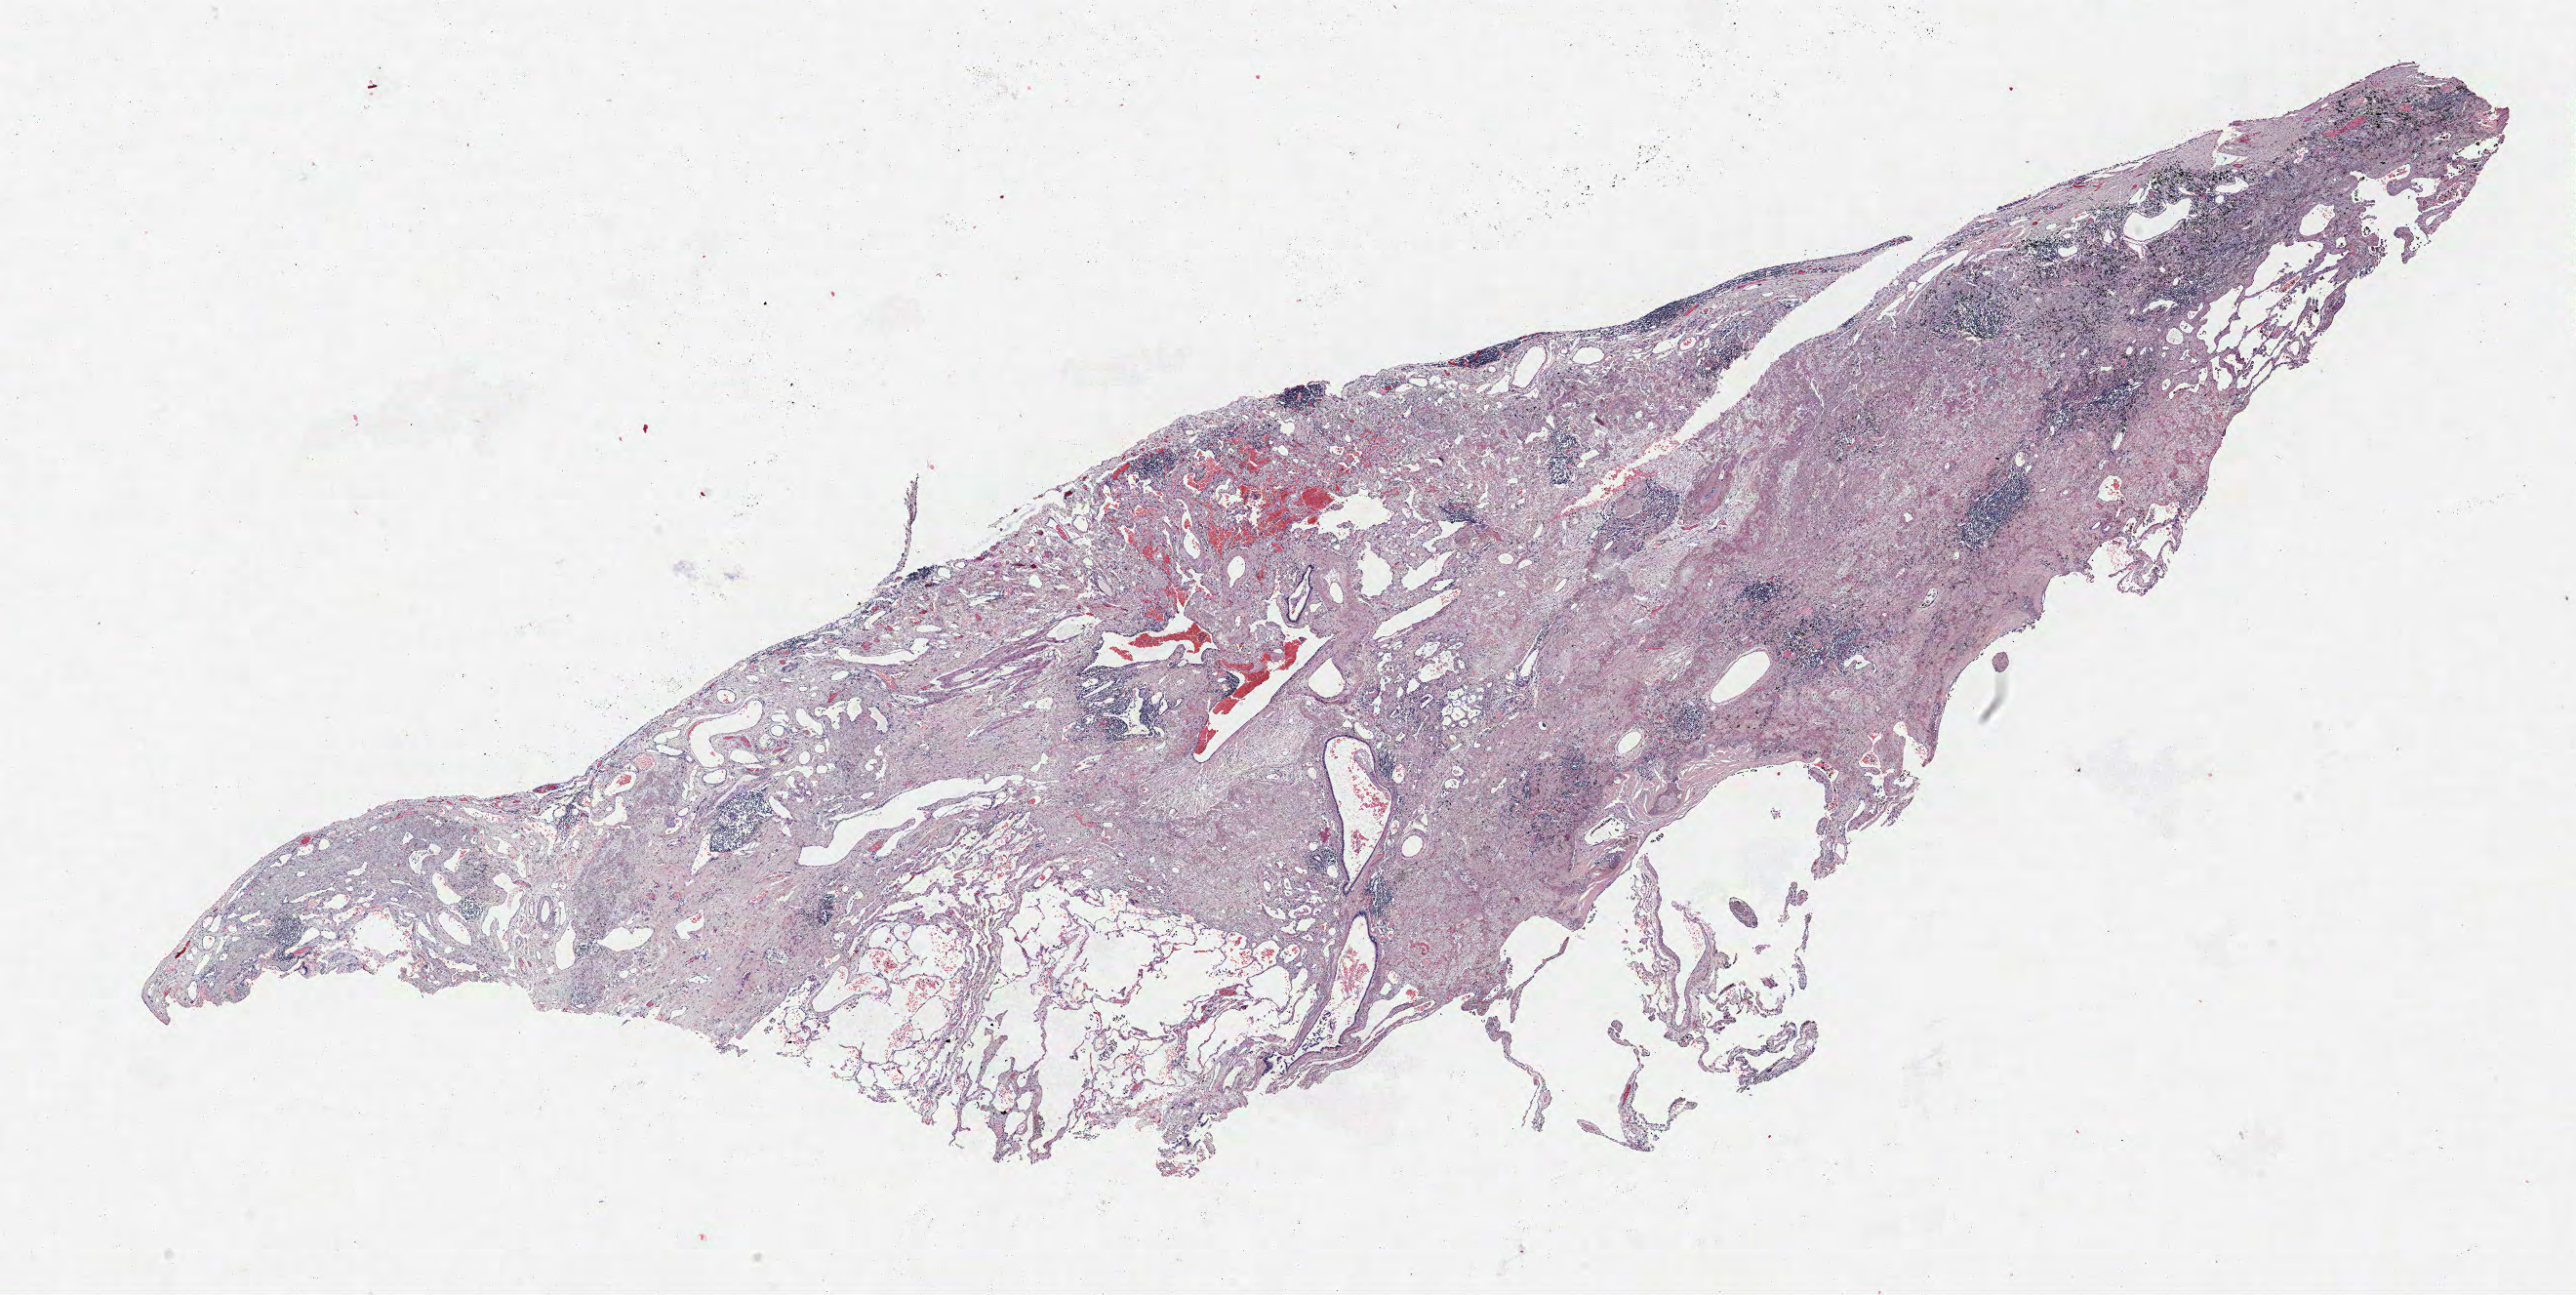
Whole-slide histology image, H&E-stained — shown as a low-resolution overview of the whole scanned area (about 21.1 x 10.6 mm). Formalin-fixed paraffin-embedded (FFPE) section. Lung. Male patient, aged 70 at enrolment. Current smoker at enrolment. Grade: poorly differentiated (G3).
* stage (AJCC 6th edition): IA
* ICD-O-3 topography: upper lobe of lung (C34.1)
* participant's lung-cancer diagnosis: Adenocarcinoma, NOS (ICD-O-3 8140/3)
* tumour size (pathology): 20 mm
* primary tumour location (clinical record): right upper lobe